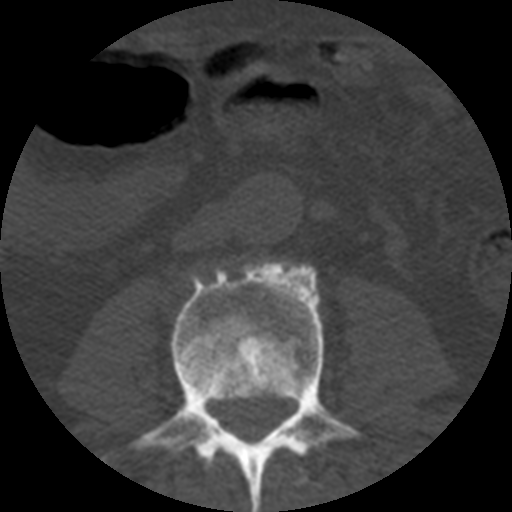
CT including the spine, one axial slice; position 120 of 508 along the scan axis; bone window (W 1800 / L 400 HU); 1.25 mm slice thickness; 512 × 512 image matrix, field of view 160 × 160 mm. Patient age 57 years. Case-level facts recorded for this patient, not image findings: primary cancer: prostate.
Outlined on this slice (semi-automatically segmented with operator editing):
- L2 vertebra: bounding box <271,444,308,486> (left, top, right, bottom; pixels)
- L3 vertebra: <130,261,361,512>